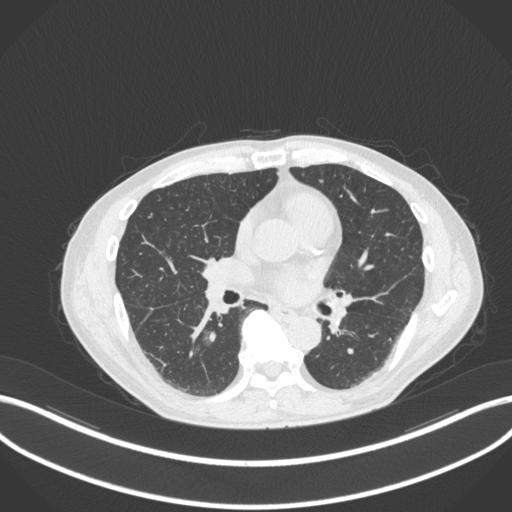
Chest CT, one axial slice. Slice 161 of 324 in the series (ordered by position). Reconstruction kernel B31f. 120 kVp. Lung window (W 1500 / L -600 HU). 1 mm slice thickness. 512 × 512 image matrix, field of view 400 × 400 mm. Patient: male, 61 years. Case-level facts recorded for this patient, not image findings: clinical TNM (as recorded): T1c N0 M0.
Annotated regions visible in this slice (bounding box drawn by a radiologist):
- lung tumour (recorded histology: adenocarcinoma): bounding box [x1, y1, x2, y2] px = [198, 325, 222, 353]